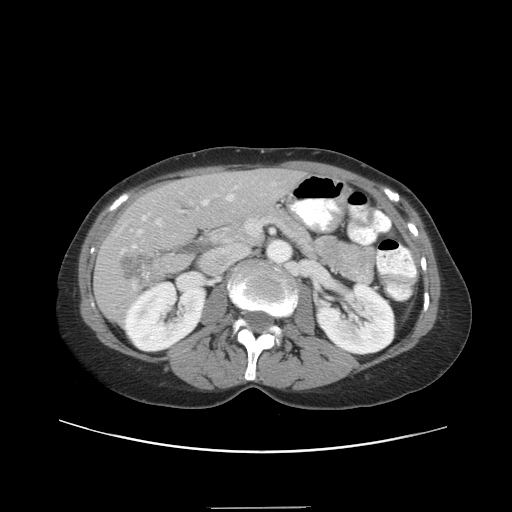
Contrast-enhanced abdominal CT, one axial slice; reconstruction kernel STANDARD; 120 kVp; intravenous contrast given; soft-tissue window (W 400 / L 40 HU); 5 mm slice thickness; 512 × 512 image matrix, field of view 388 × 388 mm. Female patient, age 64 years. From the clinical record (not read from this slice): diagnosis: colorectal cancer liver metastases, imaged before liver resection; multiple liver metastases: no; largest metastasis: 3.8 cm; disease in both lobes: yes.
Outlined on this slice (expert manual segmentation):
- hepatic veins: bounding box (x1, y1, x2, y2) in pixels: (138, 195, 234, 235)
- liver: (96, 170, 301, 321)
- planned liver remnant (the part of the liver to remain after resection): (143, 168, 301, 234)
- portal vein (with intrahepatic branches): (121, 186, 237, 253)
- liver metastasis: (121, 252, 165, 286)